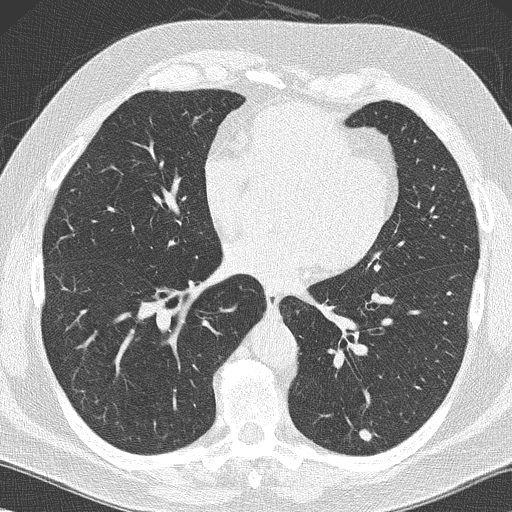
Chest CT (low-dose screening protocol), one axial image. Baseline screening round. Lung window (W 1500 / L -600 HU). Lung (sharp) reconstruction kernel (B50f). 120 kVp. Slice 93 of 152 in the series. Male participant, aged 59 years at enrolment.
• Lesion marked by an expert reader, bounding box (x1, y1, x2, y2) in pixels: (344, 417, 385, 452).
• The screening reader recorded 2 non-calcified nodules or masses ≥4 mm on this exam; which of them this box marks is not recorded.
• Participant outcome: lung cancer diagnosed 61 days after this screen — large cell carcinoma, NOS, left lower lobe, poorly differentiated (G3), stage IA (AJCC 6th edition), 14 mm at pathology.